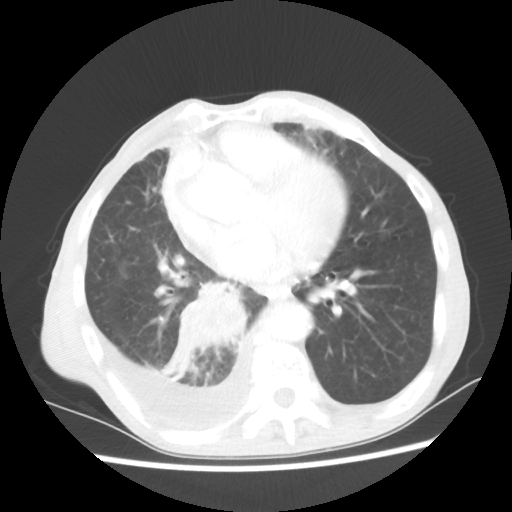
Chest CT, one axial slice. Slice 25 of 60 in the series (ordered by position). Reconstruction kernel STANDARD. Lung window (W 1500 / L -600 HU). 5 mm slice thickness. 512 × 512 image matrix, field of view 335 × 335 mm. Male patient, age 76 years. Case-level facts recorded for this patient, not image findings: clinical TNM (as recorded): T3 N3 M1a; histopathological grade: G3.
Outlined on this slice (bounding box drawn by a radiologist):
- lung tumour (recorded histology: squamous cell carcinoma): bounding box (x1, y1, x2, y2) in pixels: (153, 278, 251, 385)